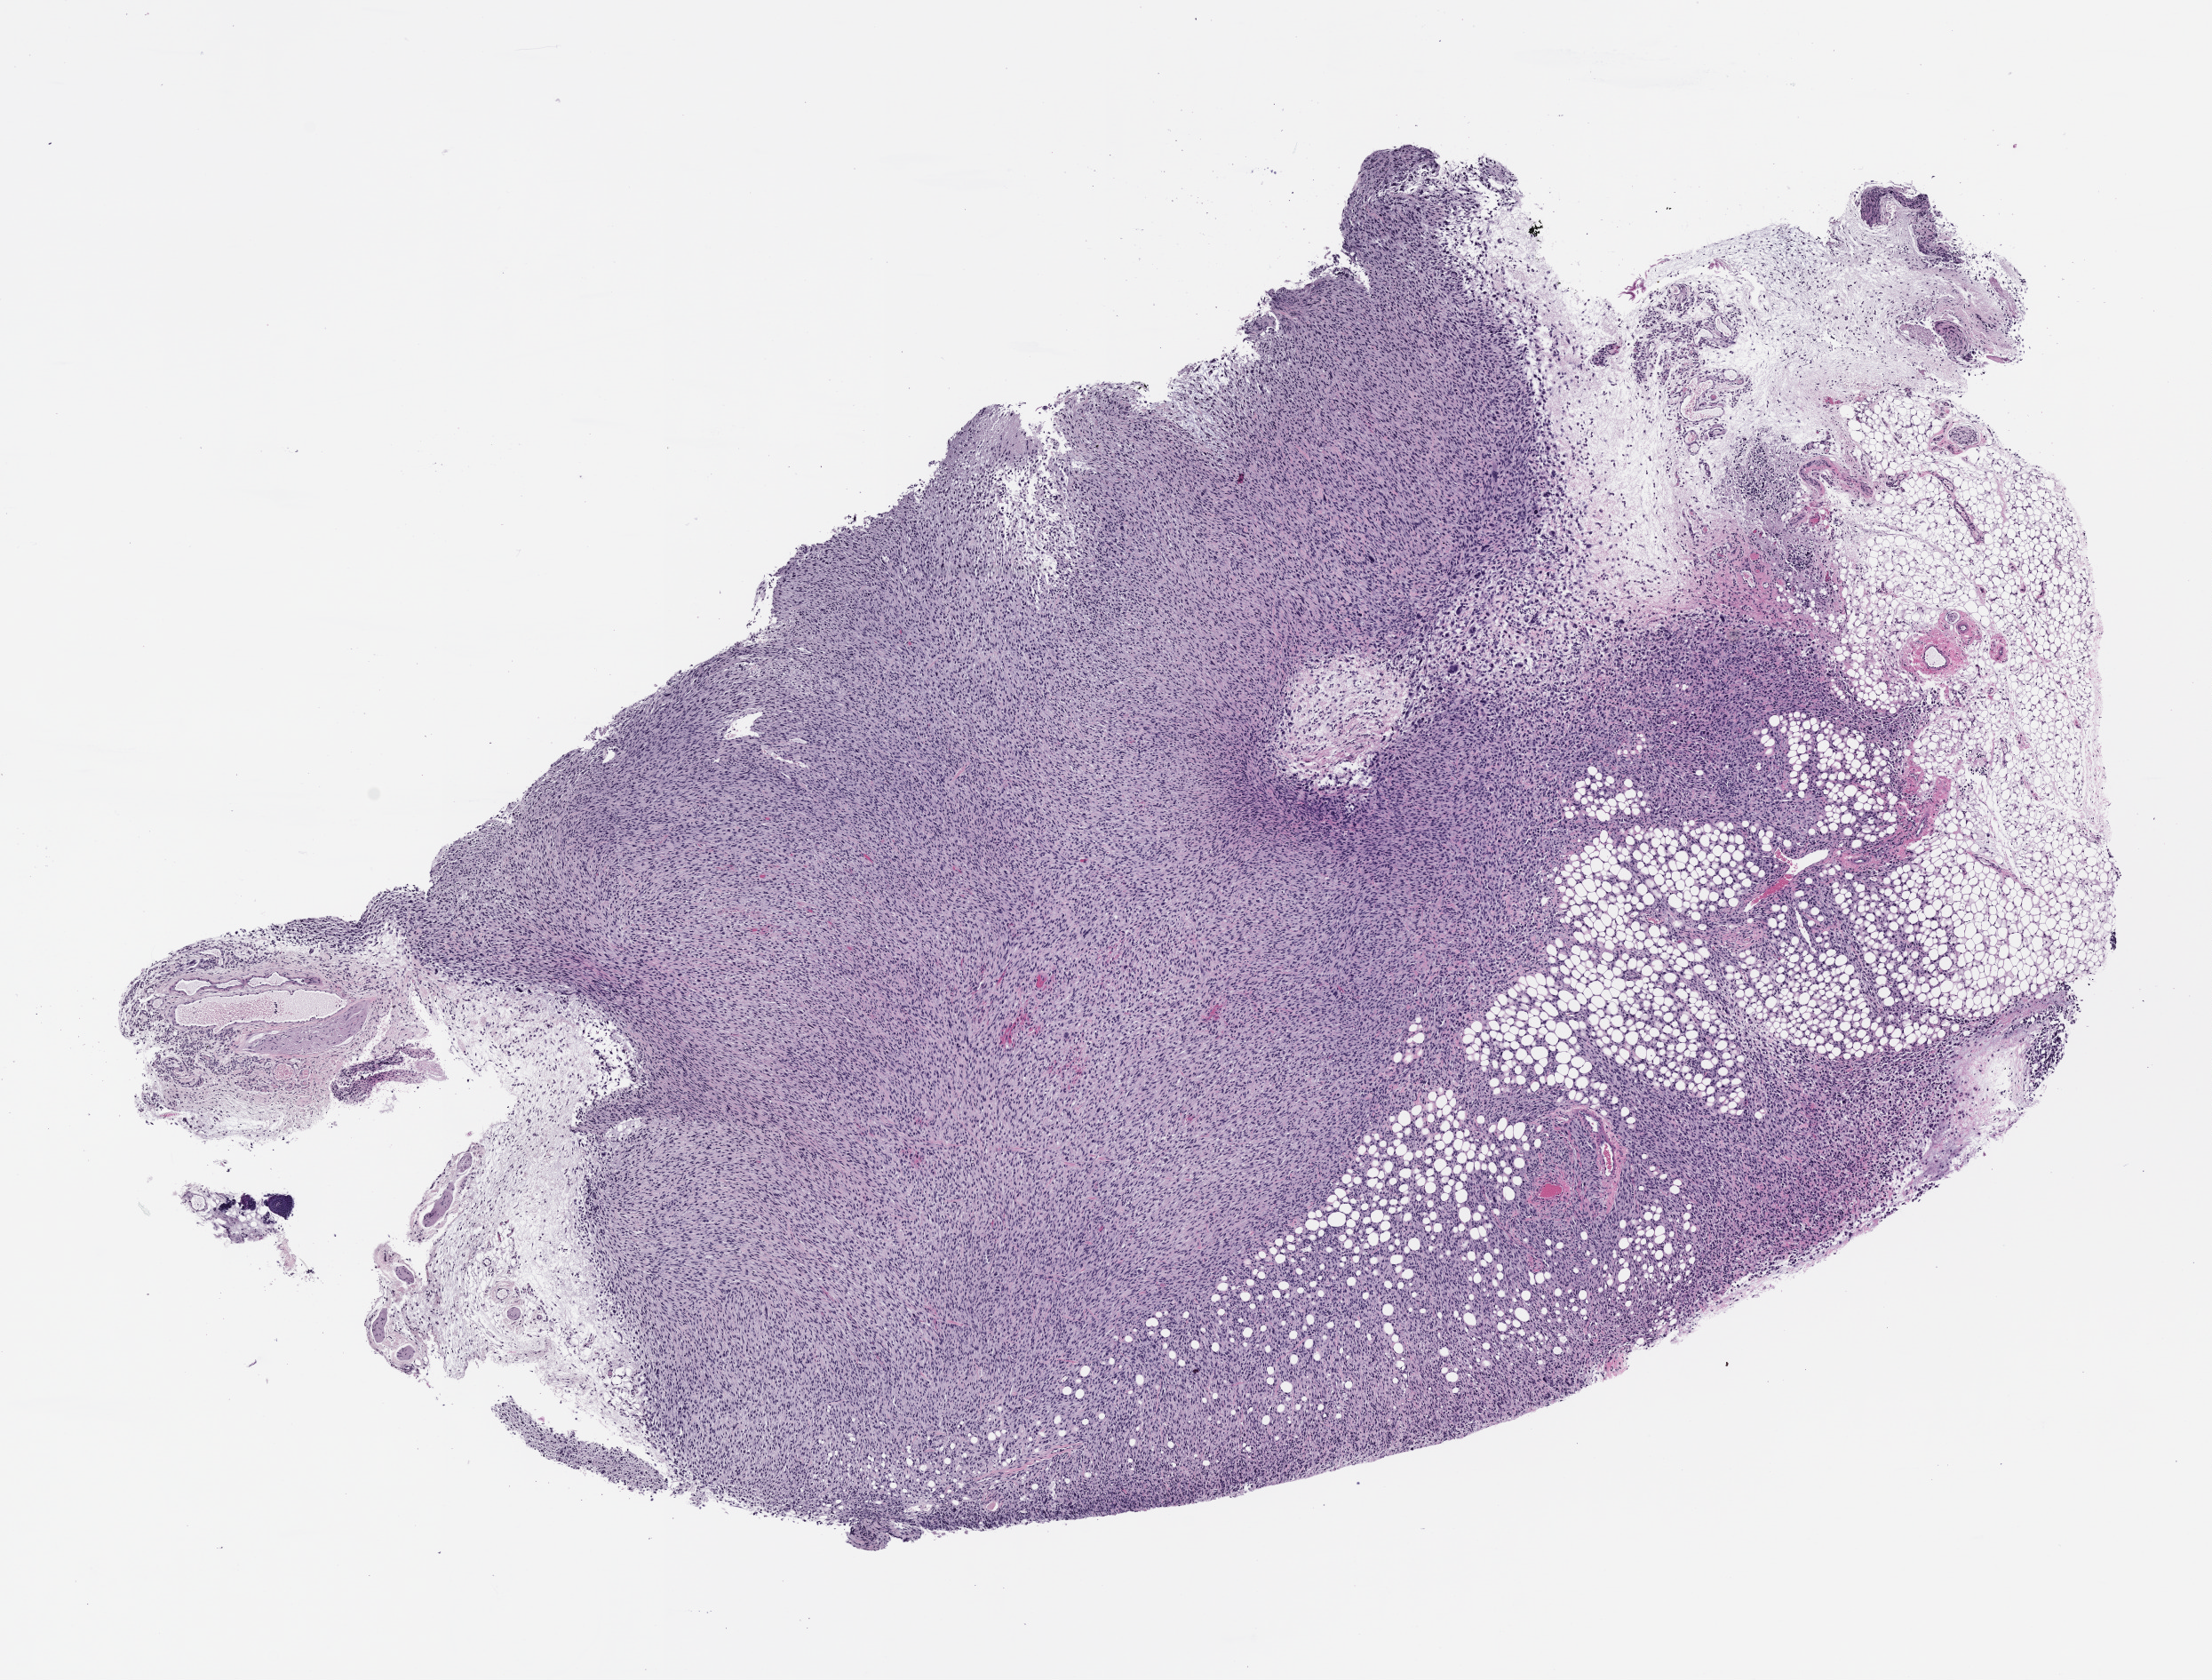
Whole-slide image, hematoxylin and eosin (H&E): patient-derived xenograft (human tumor grown in a mouse), passage 1 — shown as a low-resolution overview of the whole scanned area (about 10.0 x 7.6 mm); formalin-fixed paraffin-embedded section; tumor site category: musculoskeletal.
- originating patient diagnosis: Non-Rhabdo. soft tissue sarcoma